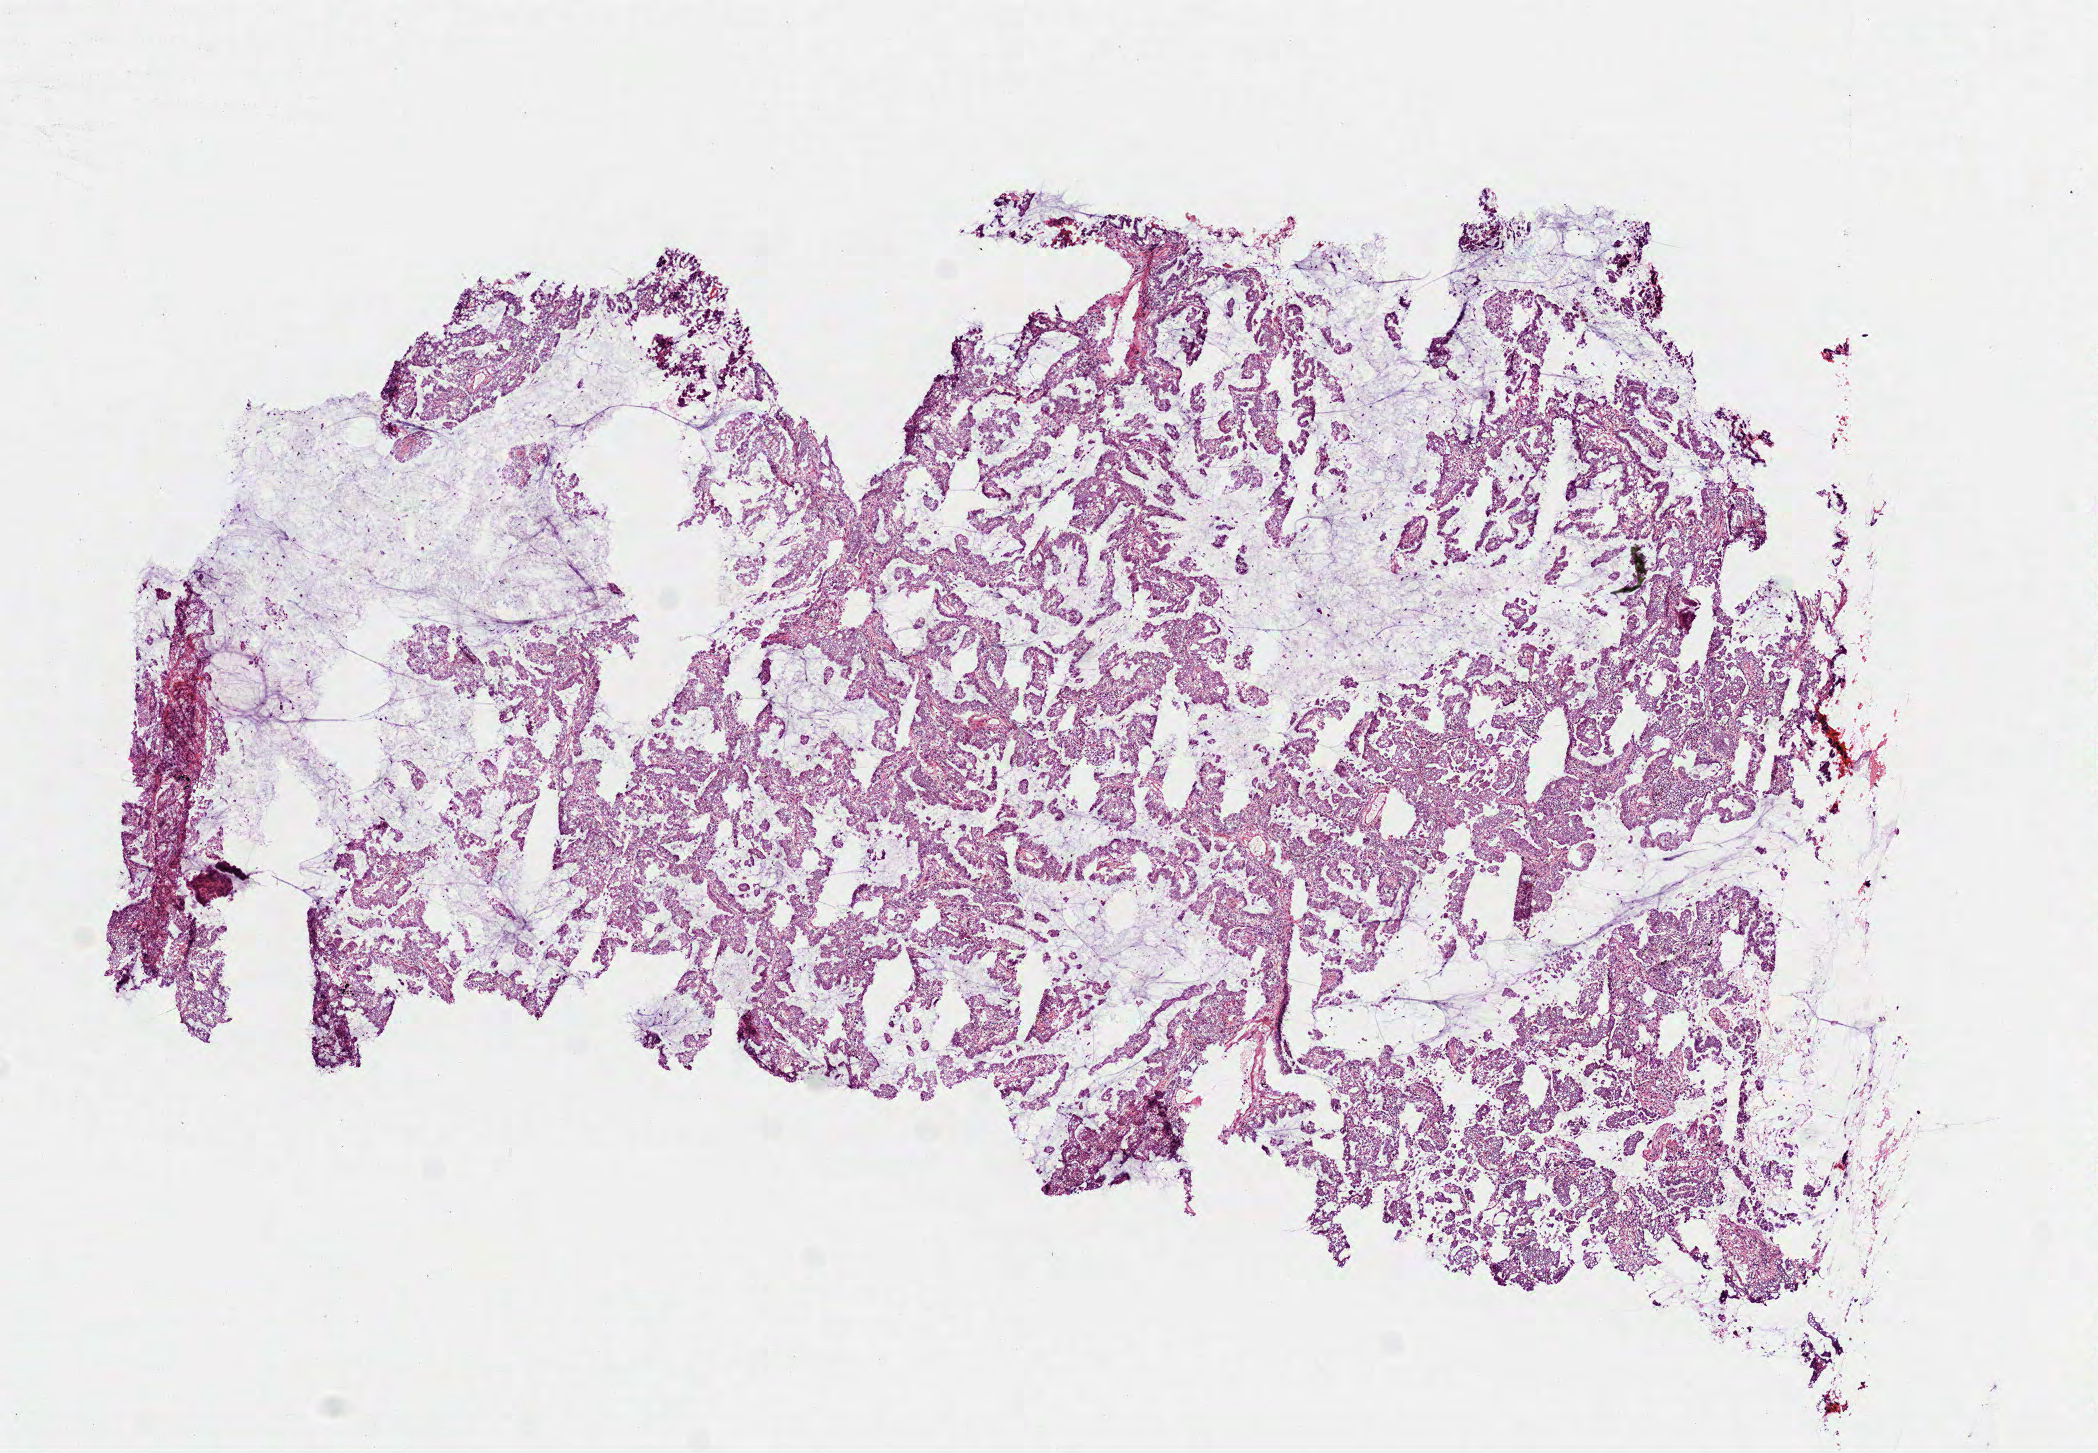
H&E-stained whole-slide image, low-resolution overview of the scanned area, about 8.5 x 5.9 mm. Frozen section from the top of the tissue portion. Lung, primary tumour sample. Male patient; age at initial diagnosis 71 years. Slide review estimates, as recorded: tumour cells 85%, tumour nuclei 70%, normal cells 0%, stromal cells 15%, necrosis 0%.
* AJCC pathologic stage: IIB (6th edition)
* laterality: left
* histologic diagnosis: Adenocarcinoma with mixed subtypes (upper lobe, lung)